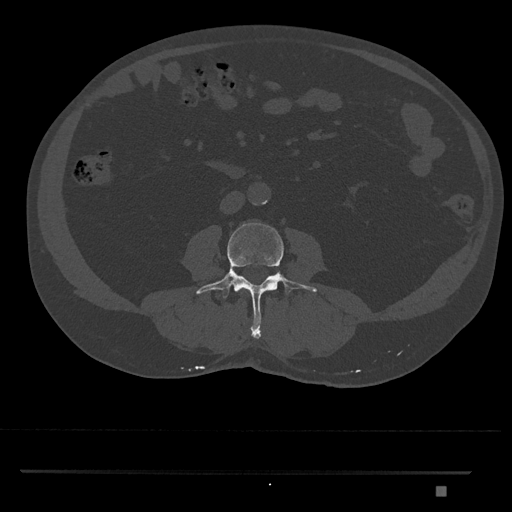
CT including the spine, one axial slice; position 680 of 1134 along the scan axis; 120 kVp; bone window (W 1800 / L 400 HU); 512 × 512 image matrix, field of view 429 × 429 mm. Patient: male, 65 years. From the clinical record (not read from this slice): primary cancer: prostate.
Outlined on this slice (semi-automatically segmented with operator editing):
- L3 vertebra: bounding box <196,222,317,339> (left, top, right, bottom; pixels)